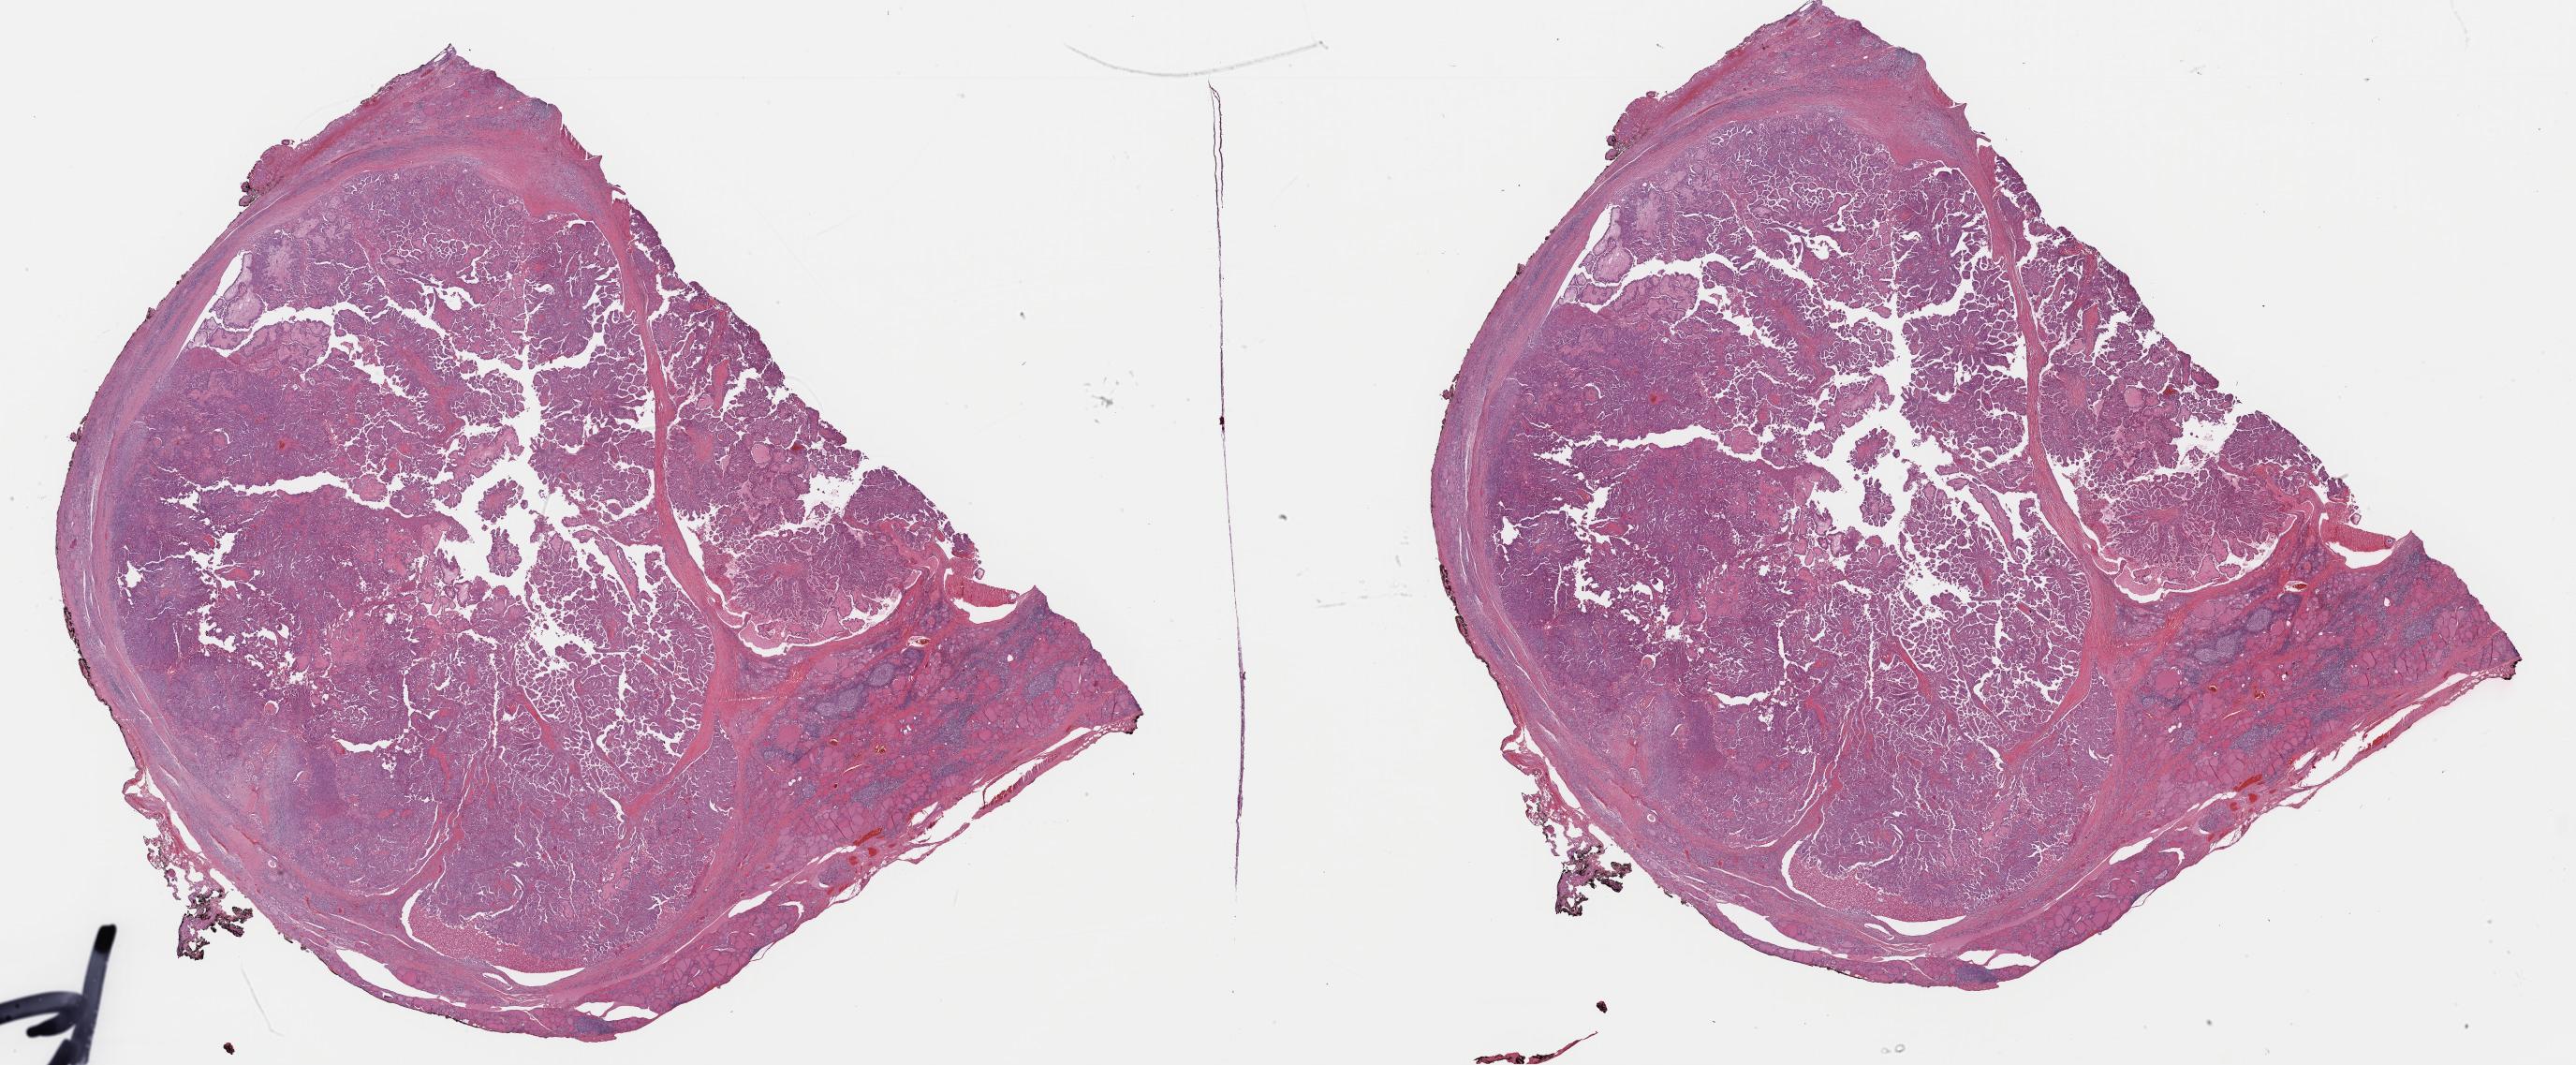
Whole-slide histology image, Hematoxylin and eosin (H&E) stained, whole scanned area (about 43.5 x 18.0 mm, from a 40x scan) shown as a low-resolution overview; formalin-fixed paraffin-embedded (FFPE) diagnostic section; sample: primary tumour, thyroid. Female patient; age at initial diagnosis 39 years.
Lymph nodes positive (case pathology): 5 of 14 examined. Pathologic diagnosis: Papillary adenocarcinoma, NOS (thyroid gland). AJCC pathologic stage: I (7th edition). Laterality: bilateral.